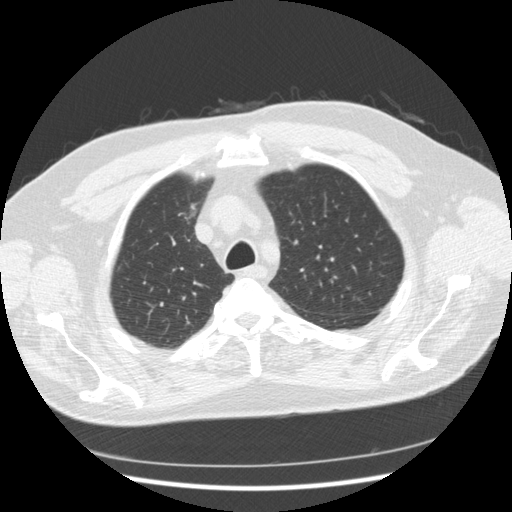
Chest CT (low-dose screening protocol), one axial image; second annual screen; lung window (W 1500 / L -600 HU); slice 47 of 267 in the series. Male participant, aged 66 years at enrolment. Former smoker at enrolment.
Expert-annotated lung lesion, box from (x=158, y=196) to (x=214, y=240) px. No non-calcified nodule or mass ≥4 mm was recorded by the screening reader at this exam. Official screen result: positive, other.